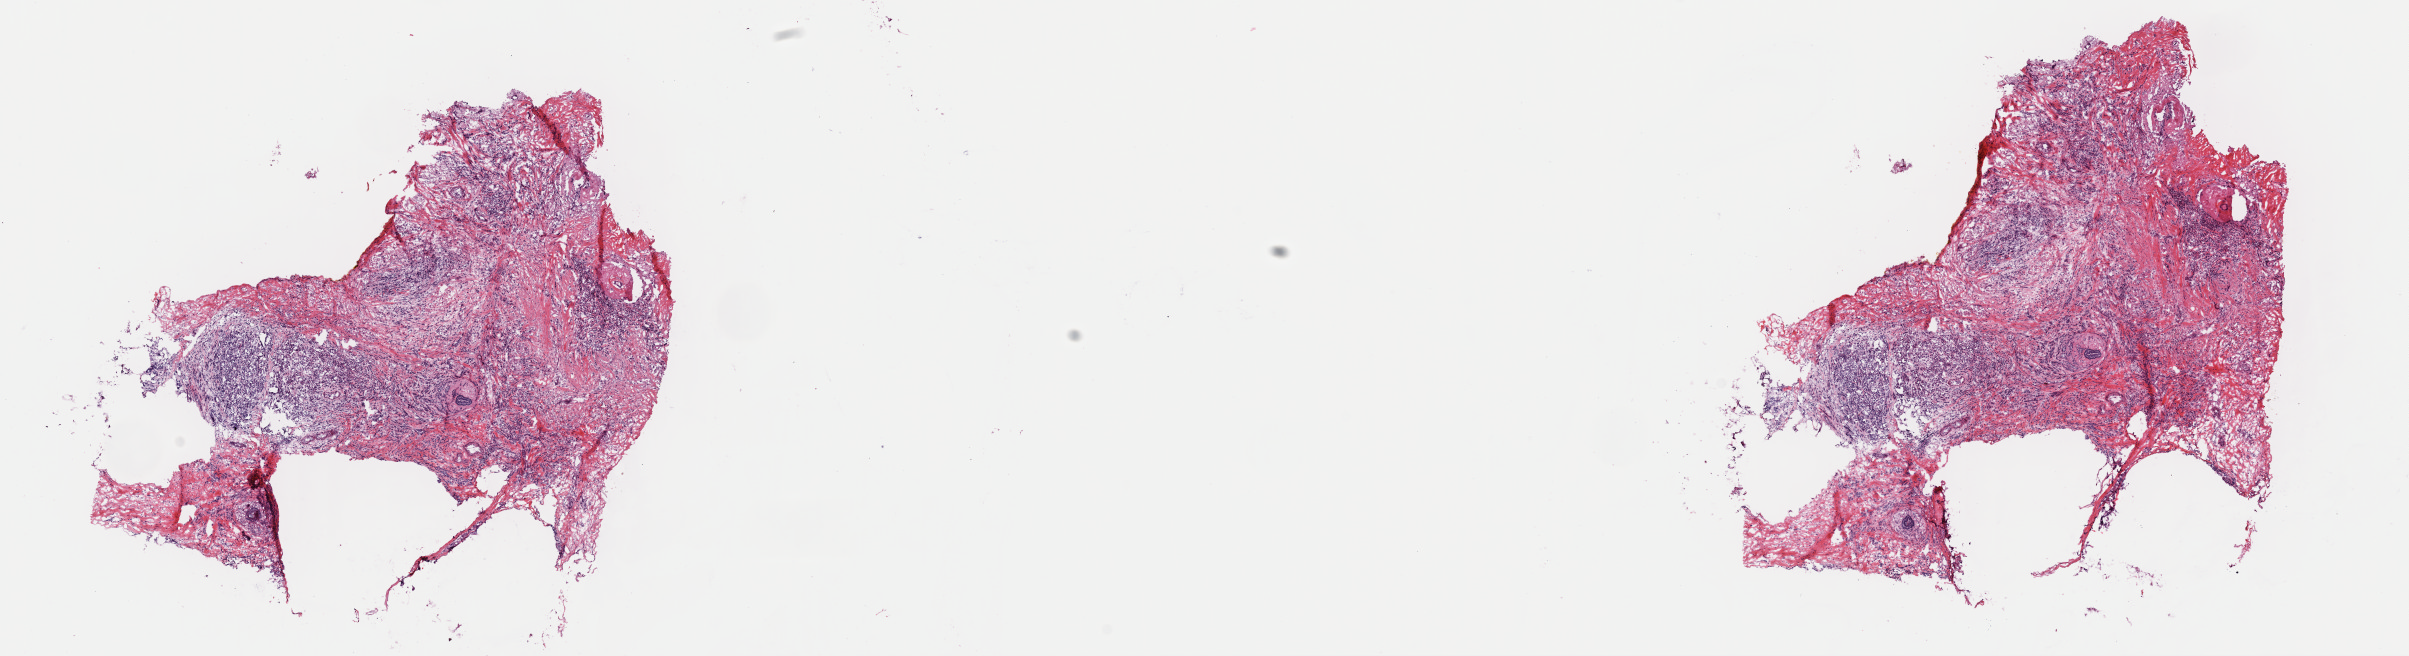
Digitized H&E tissue section (whole slide), whole scanned area (about 19.0 x 5.2 mm) shown as a low-resolution overview, frozen section from the top of the tissue portion, primary tumour sample from the breast. Female patient; age at initial diagnosis 47 years. Composition of this section per pathologist review: tumour cells 95%, tumour nuclei 60%, normal cells 5%, stromal cells 0%, necrosis 0%. Infiltration values recorded for this section: lymphocyte infiltration 5%, monocyte infiltration 0%, neutrophil infiltration 0%.
- laterality: right
- AJCC pathologic stage: IIB (7th edition)
- diagnosis: Infiltrating lobular mixed with other types of carcinoma
- lymph nodes positive (case pathology): 1 of 1 examined